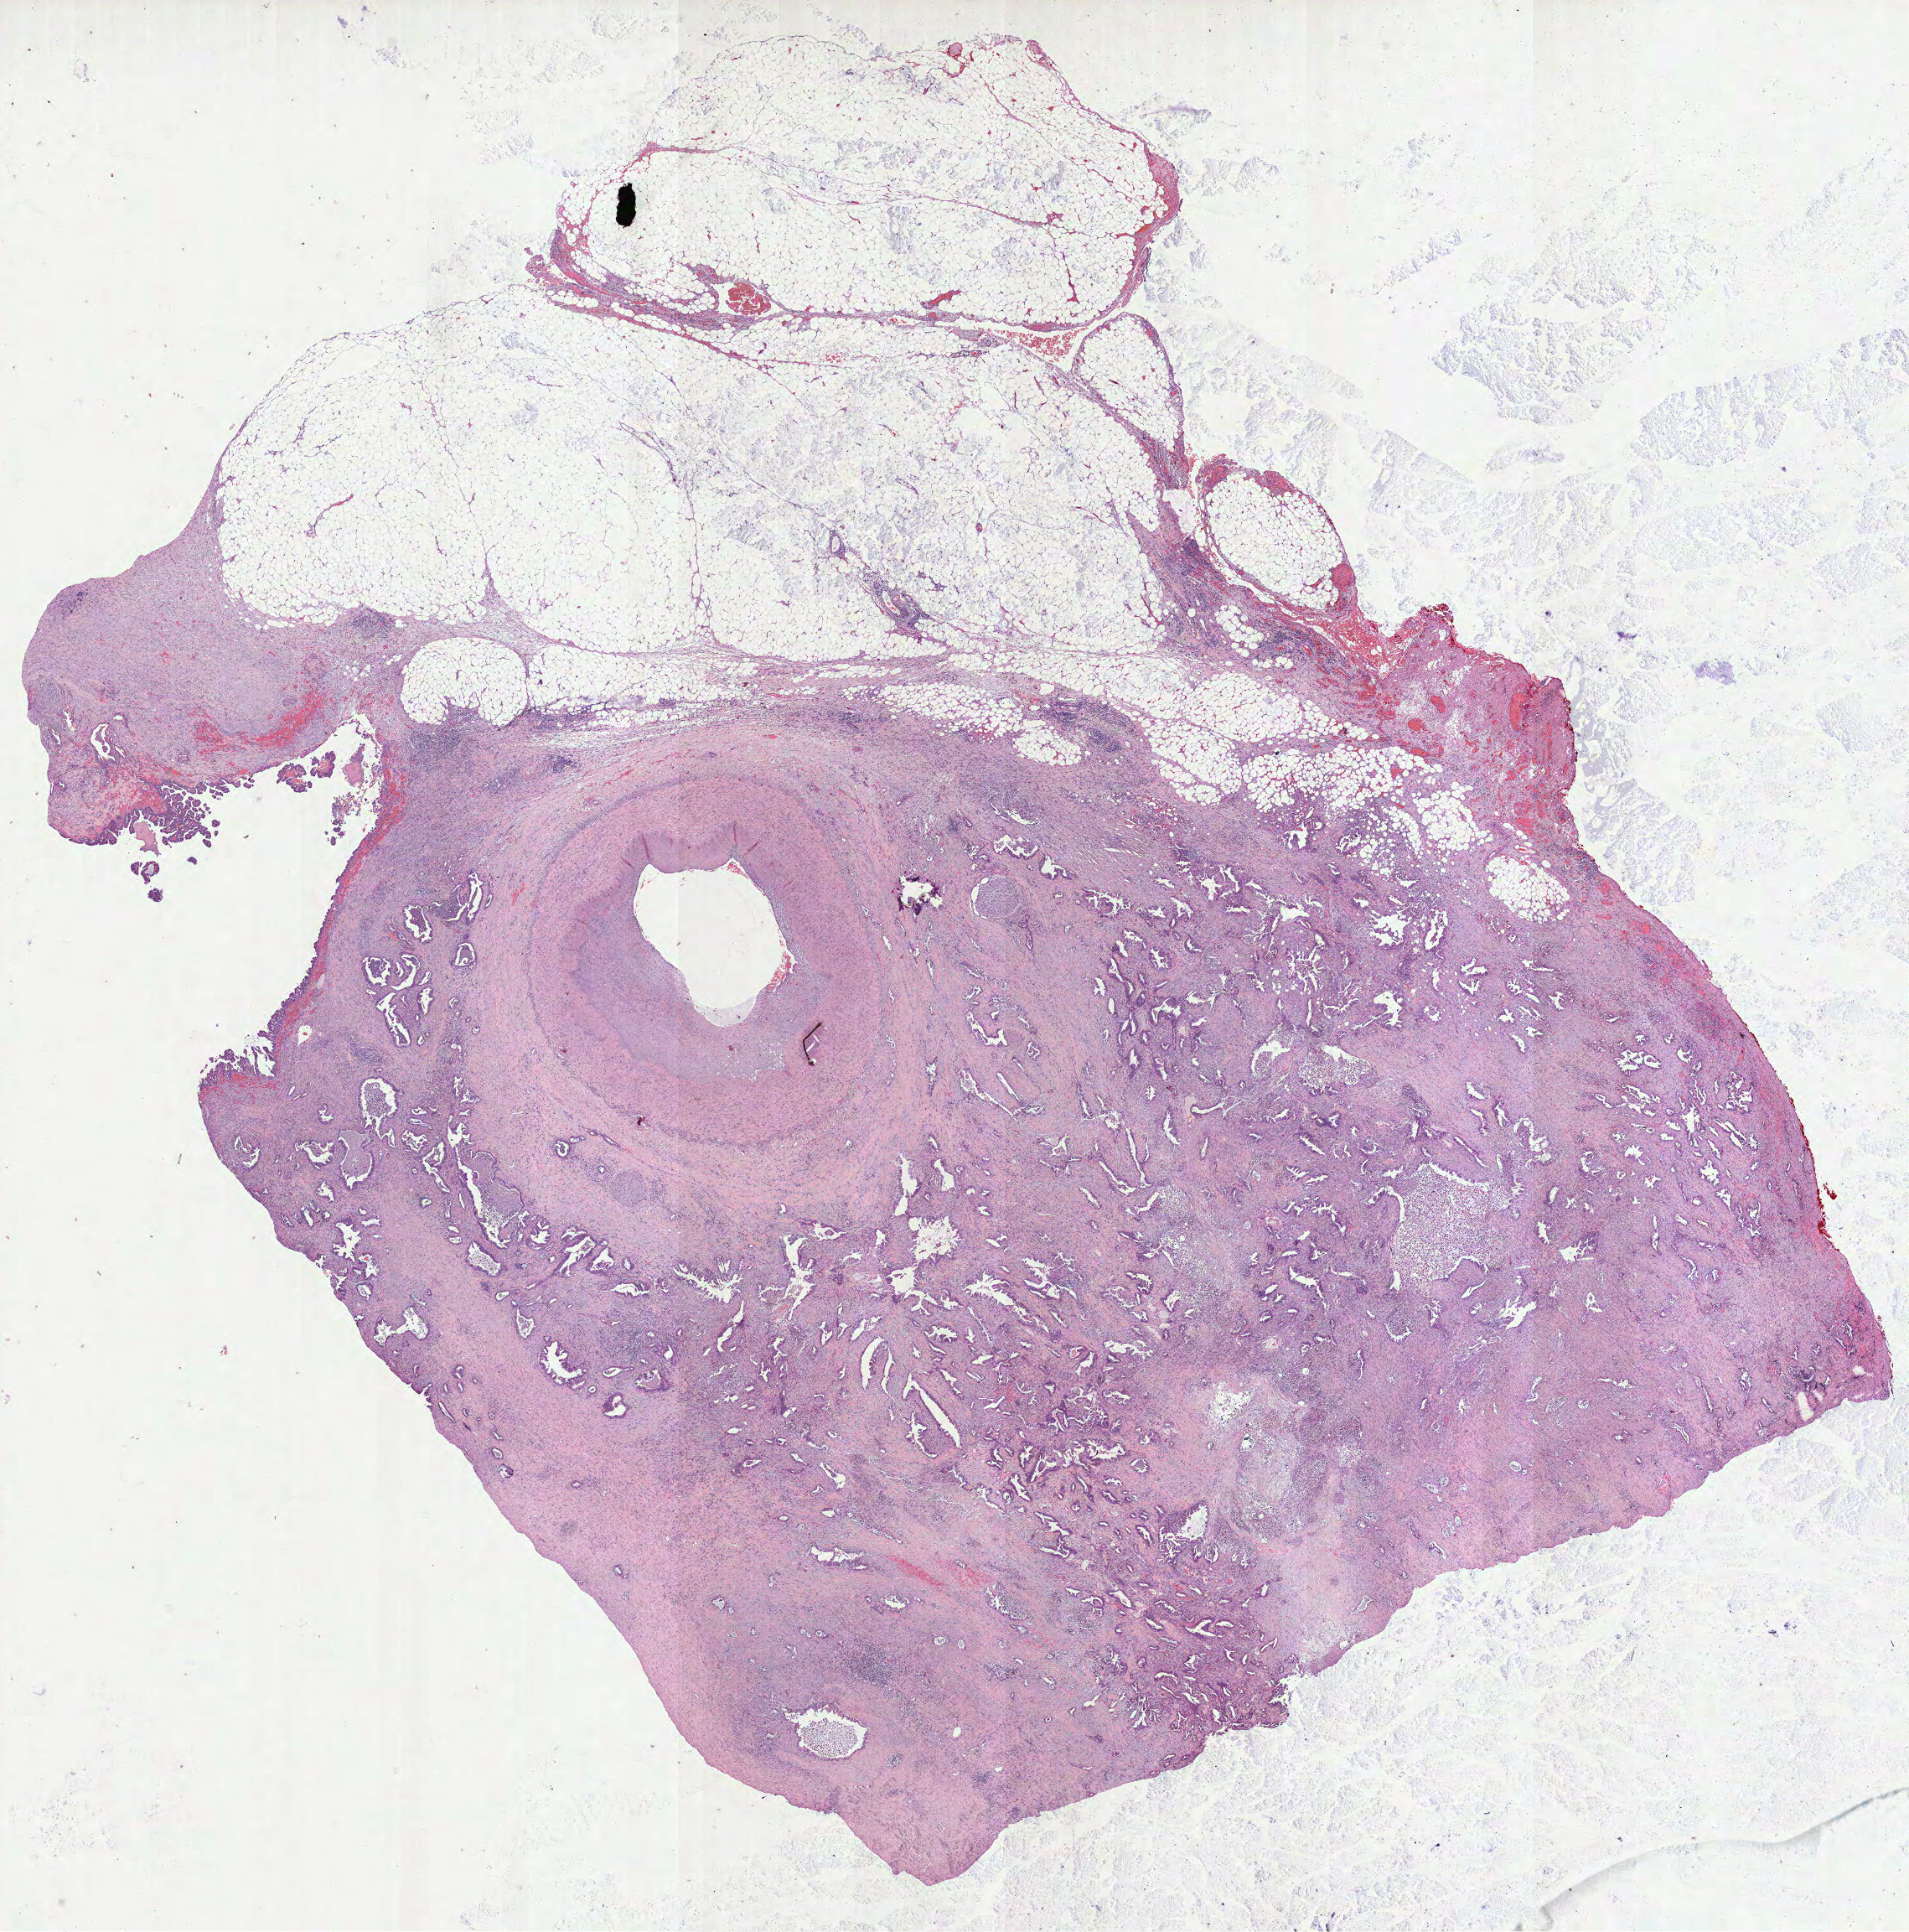
H&E-stained whole-slide image — whole scanned area (about 18.4 x 18.6 mm) shown as a low-resolution overview. Formalin-fixed paraffin-embedded (FFPE) diagnostic section. Pancreas, primary tumour sample. Patient: female, age at initial diagnosis 58 years. Histologic grade: G3 (poorly differentiated).
Diagnosis: Infiltrating duct carcinoma, NOS (tail of pancreas). Lymph nodes positive (case pathology): 0 of 2 examined. AJCC pathologic stage: IV.